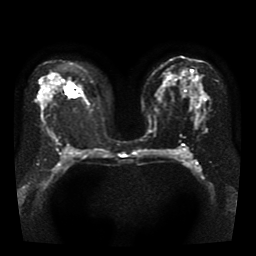
Breast MRI, one axial slice; position 24 of 41 along the scan axis; diffusion-weighted series; image 2 of 4 stored at this slice position (different b-values; order by instance number); 1.5 T; 5 mm slice thickness; 256 × 256 image matrix. Female patient.
Outlined on this slice (expert manual segmentation):
- tumour on diffusion-weighted imaging: bounding box [x1, y1, x2, y2] px = [65, 86, 78, 97]